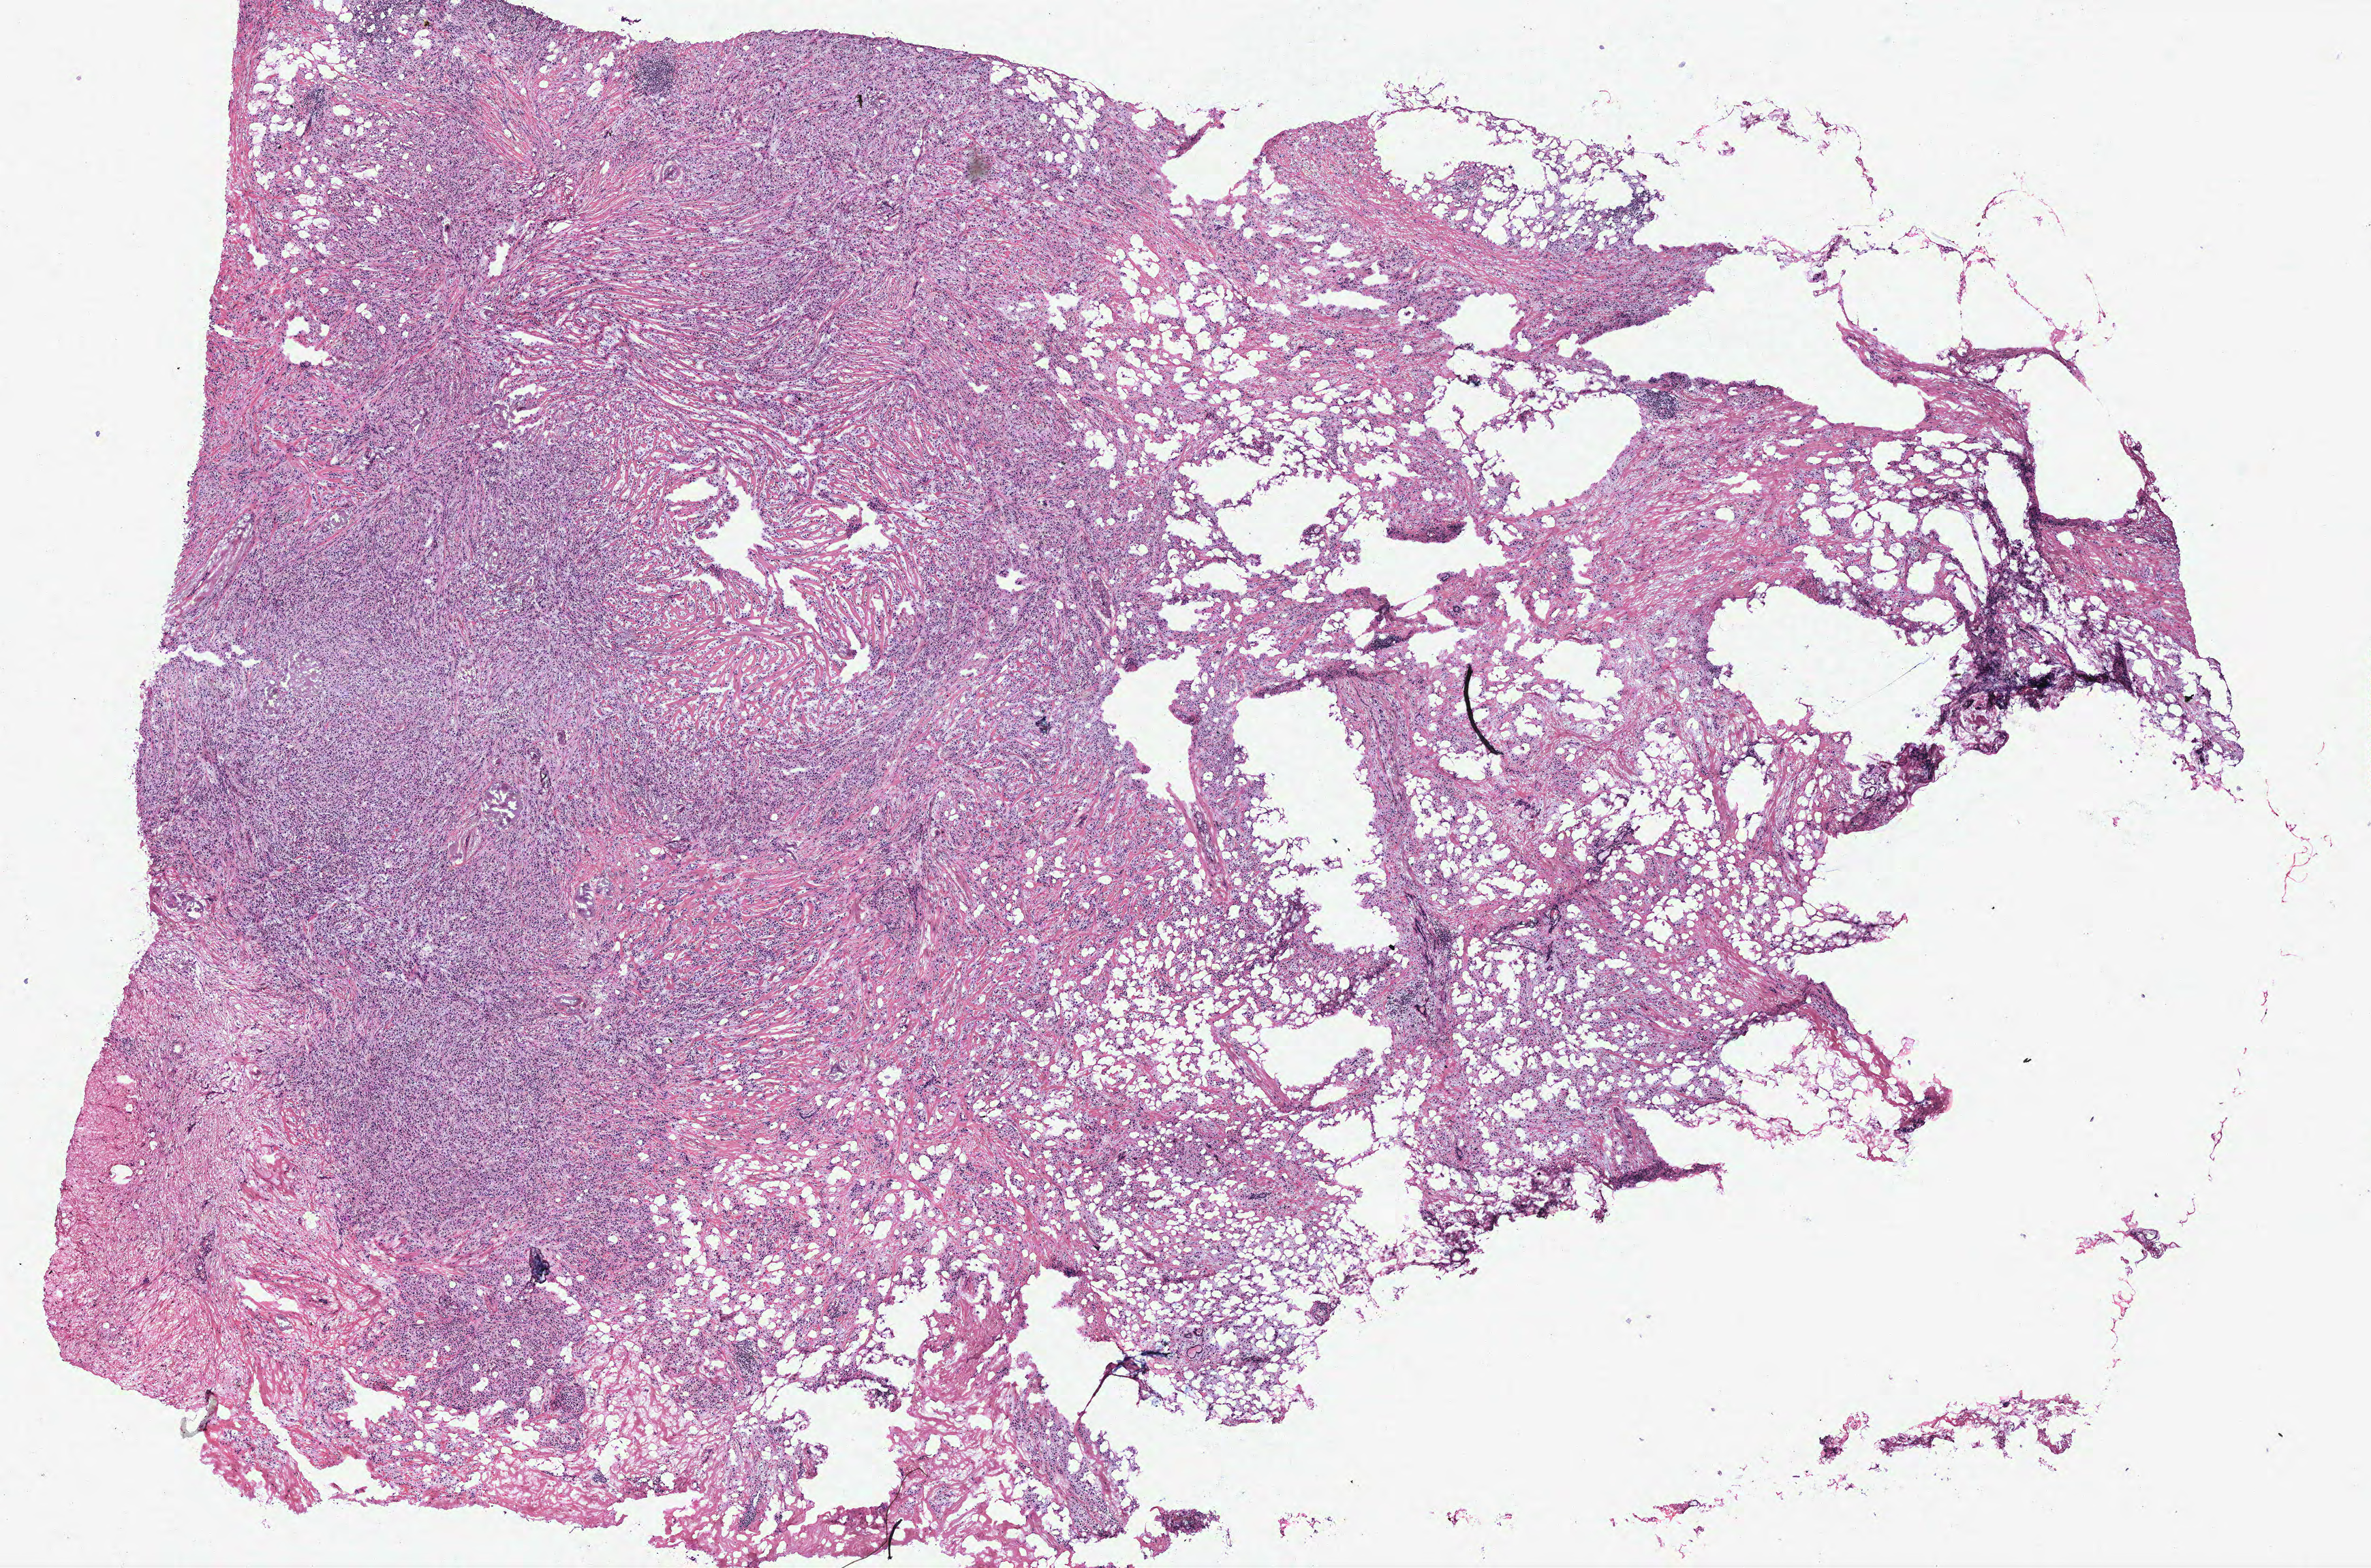
H&E-stained whole-slide image — shown as a low-resolution overview of the whole scanned area (about 13.9 x 9.2 mm, acquisition: 40x scan); breast, tumour tissue. 74-year-old female patient.
Diagnosis: Infiltrating duct carcinoma, NOS.